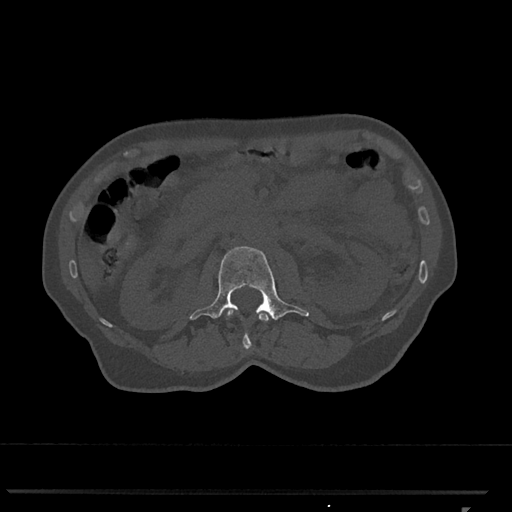
CT including the spine, one axial slice; slice 352 of 793 in the series (ordered by position); reconstruction kernel Br40s/3; bone window (W 1800 / L 400 HU); 512 × 512 image matrix, field of view 380 × 380 mm. Patient: female, 62 years. From the clinical record (not read from this slice): primary cancer: renal.
Outlined on this slice (semi-automatic segmentation, software-assisted and operator-edited):
- L1 vertebra: bounding box [x1, y1, x2, y2] px = [226, 310, 269, 349]
- L2 vertebra: [190, 246, 309, 321]